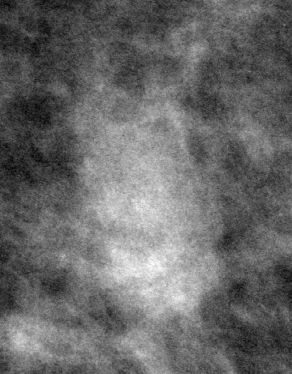
Region of interest cut from a scanned film mammogram (one marked finding), left breast, MLO view, BI-RADS breast density category 1 (scale 1–4).
Marked abnormality: mass, shape oval, margins circumscribed; BI-RADS assessment category 3; subtlety rating 5 on a 1 (subtle) to 5 (obvious) scale; benign without callback (not worked up further).